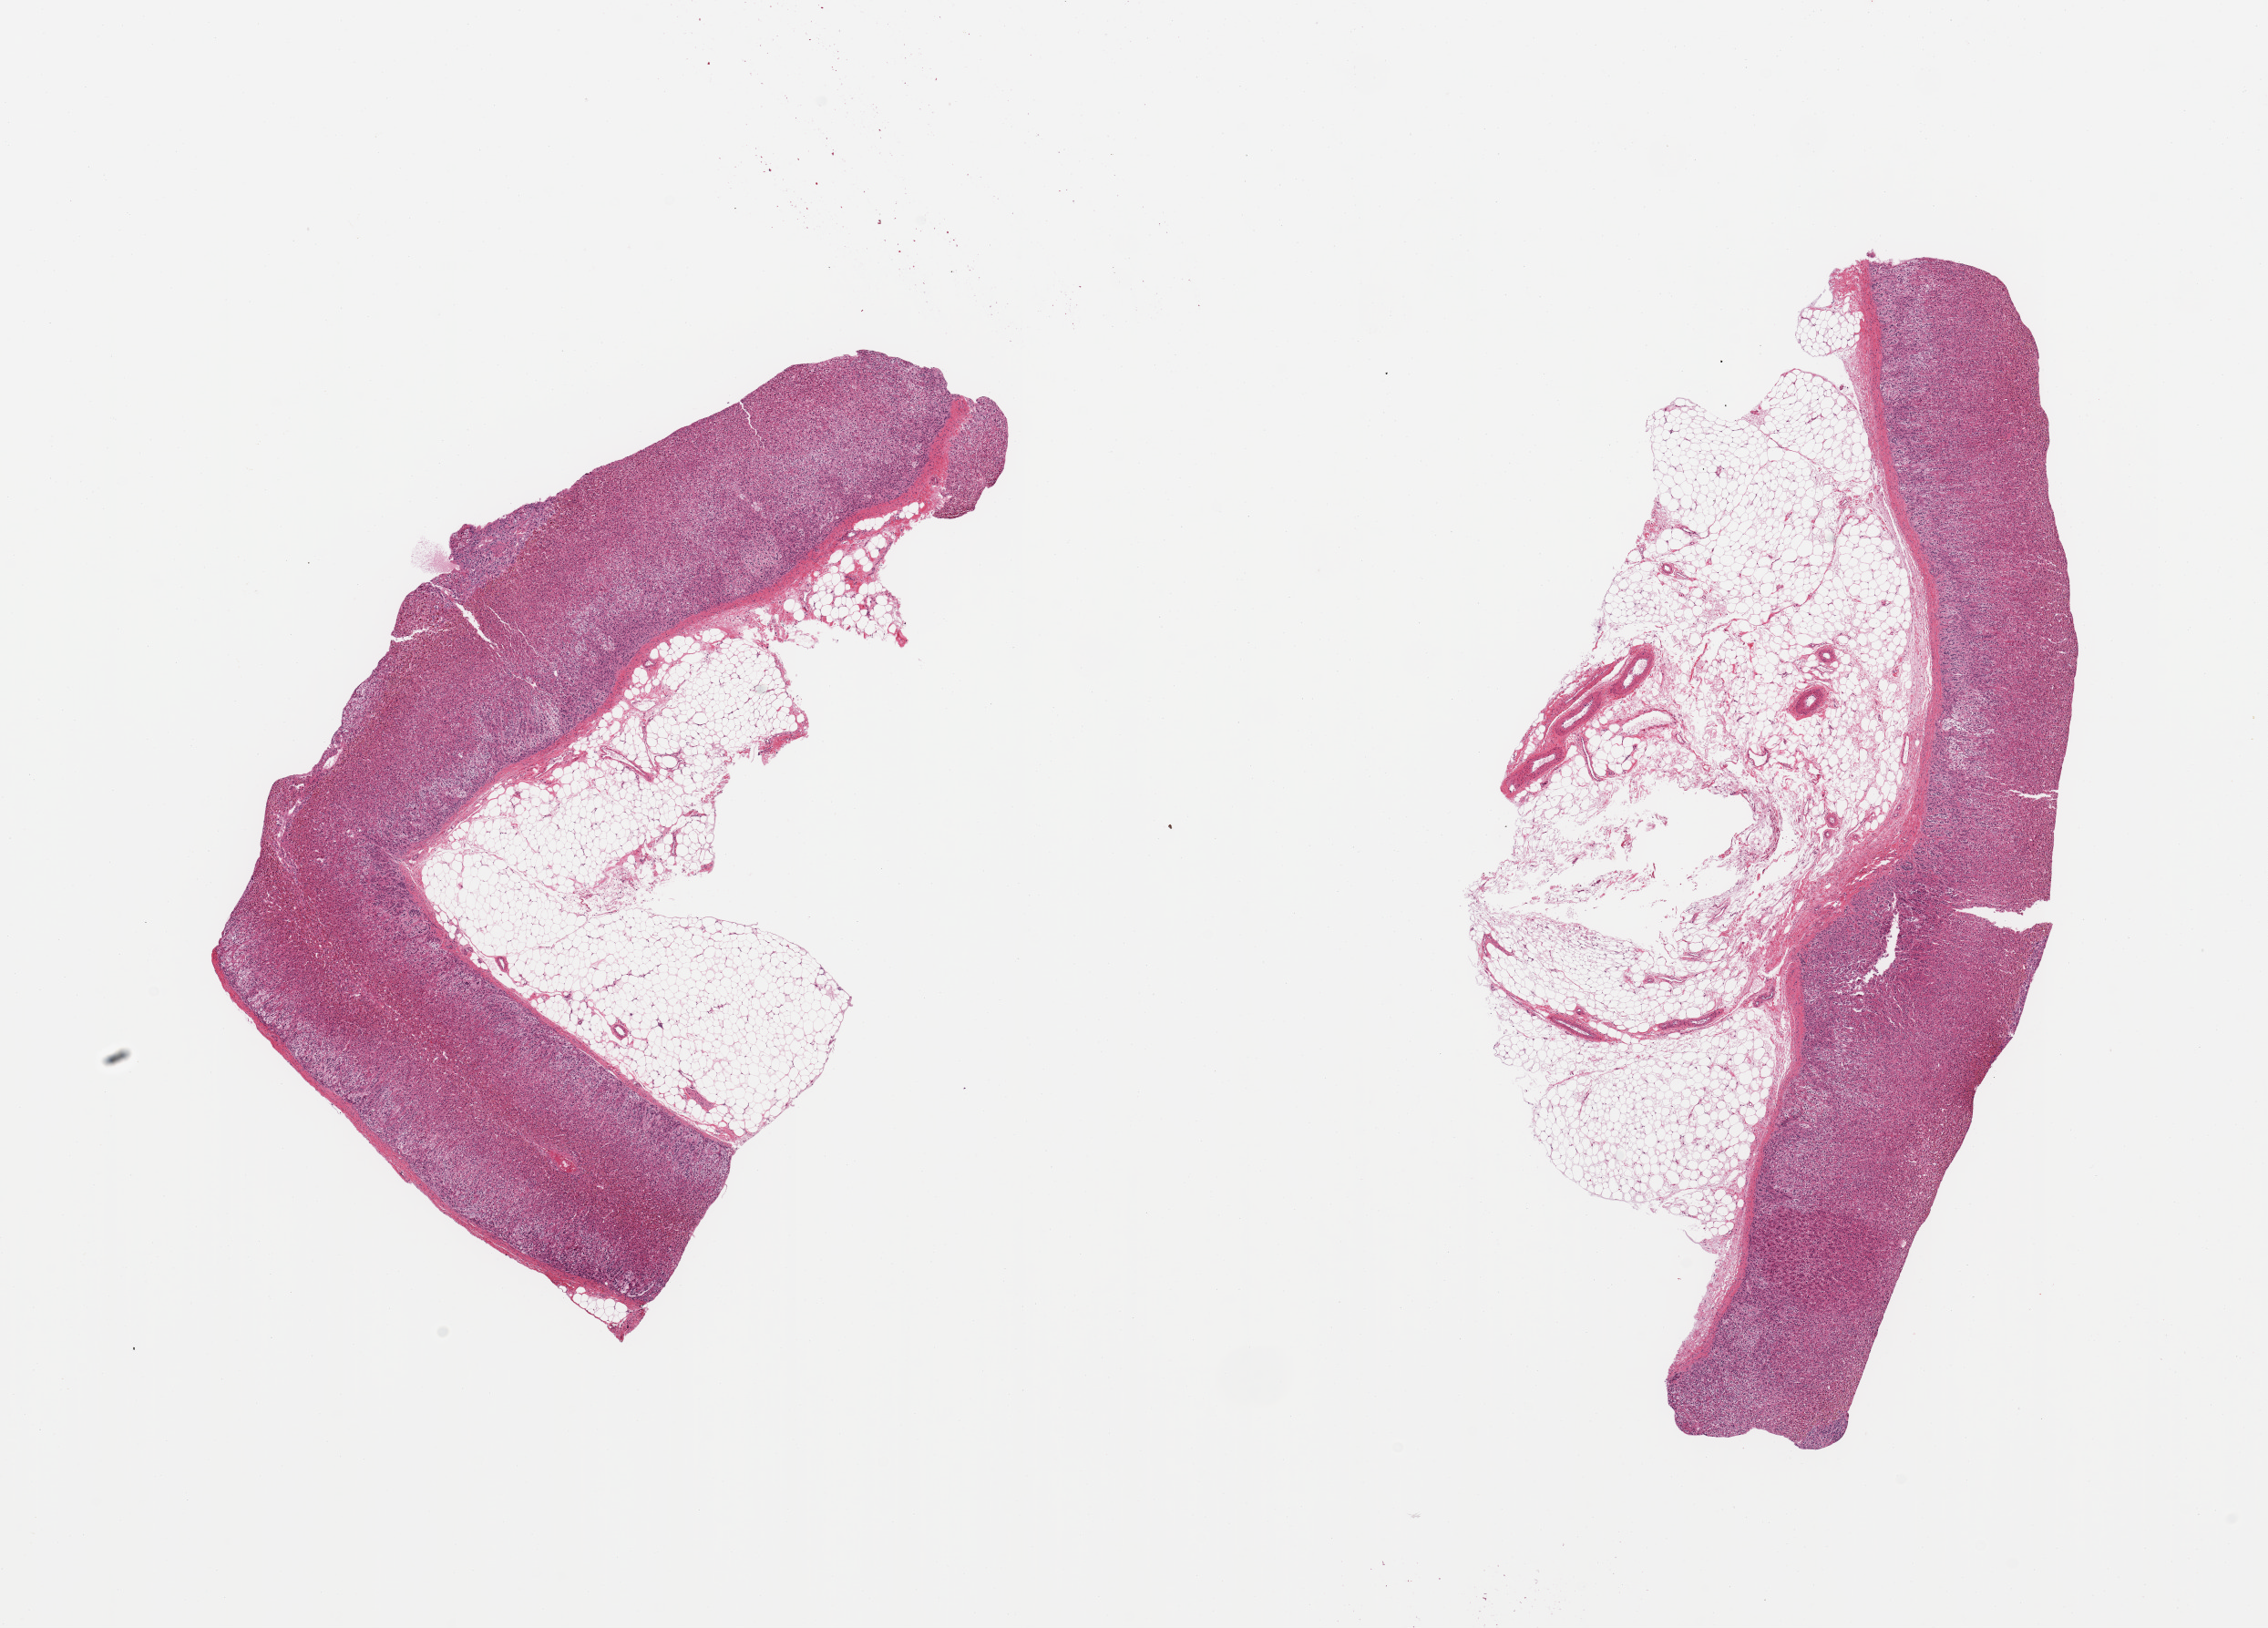
Digitized H&E-stained section, brightfield — whole scanned area (about 19.7 x 14.1 mm, acquisition: 20x scan) shown as a low-resolution overview. PAXgene-fixed, paraffin-embedded tissue. Section of adrenal gland (target tissue). Tissue donor sample. Donor sex: male.
Pathologist's review note for this sample: 2 pieces; cortex with up to 3mm external adherent fat.